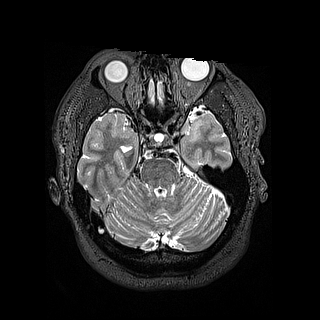
Brain MRI from a brain-tumour surgery series, one axial slice. 1.2 mm slice thickness. 320 × 320 image matrix, field of view 254 × 254 mm. From the clinical record (not read from this slice): histopathology: Astrocytoma; WHO grade: 2; IDH mutation: yes.
Outlined on this slice (manually delineated by an expert):
- tumour: box from (x=189, y=125) to (x=201, y=143) px